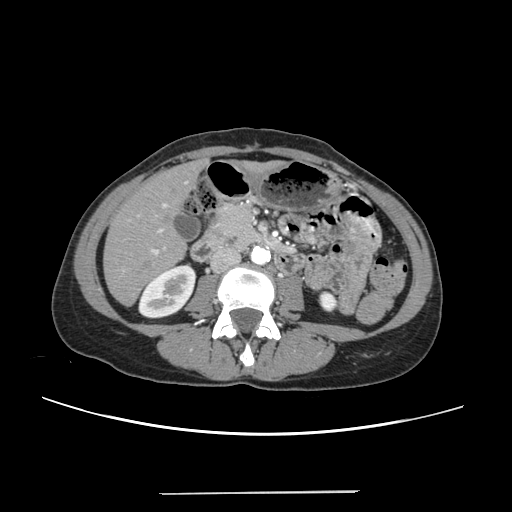
Contrast-enhanced abdominal CT, one axial slice. Position 82 of 240 along the scan axis. Intravenous contrast given. Soft-tissue window (W 400 / L 40 HU). 512 × 512 image matrix. Female patient, age 60 years. Case-level facts recorded for this patient, not image findings: diagnosis: colorectal cancer liver metastases, imaged before liver resection; multiple liver metastases: no; largest metastasis: 1.5 cm; disease in both lobes: no.
Outlined on this slice (manually delineated by an expert):
- liver: bounding box <105,163,200,304> (left, top, right, bottom; pixels)
- planned liver remnant (the part of the liver to remain after resection): <105,172,186,304>
- portal vein (with intrahepatic branches): <122,203,167,271>